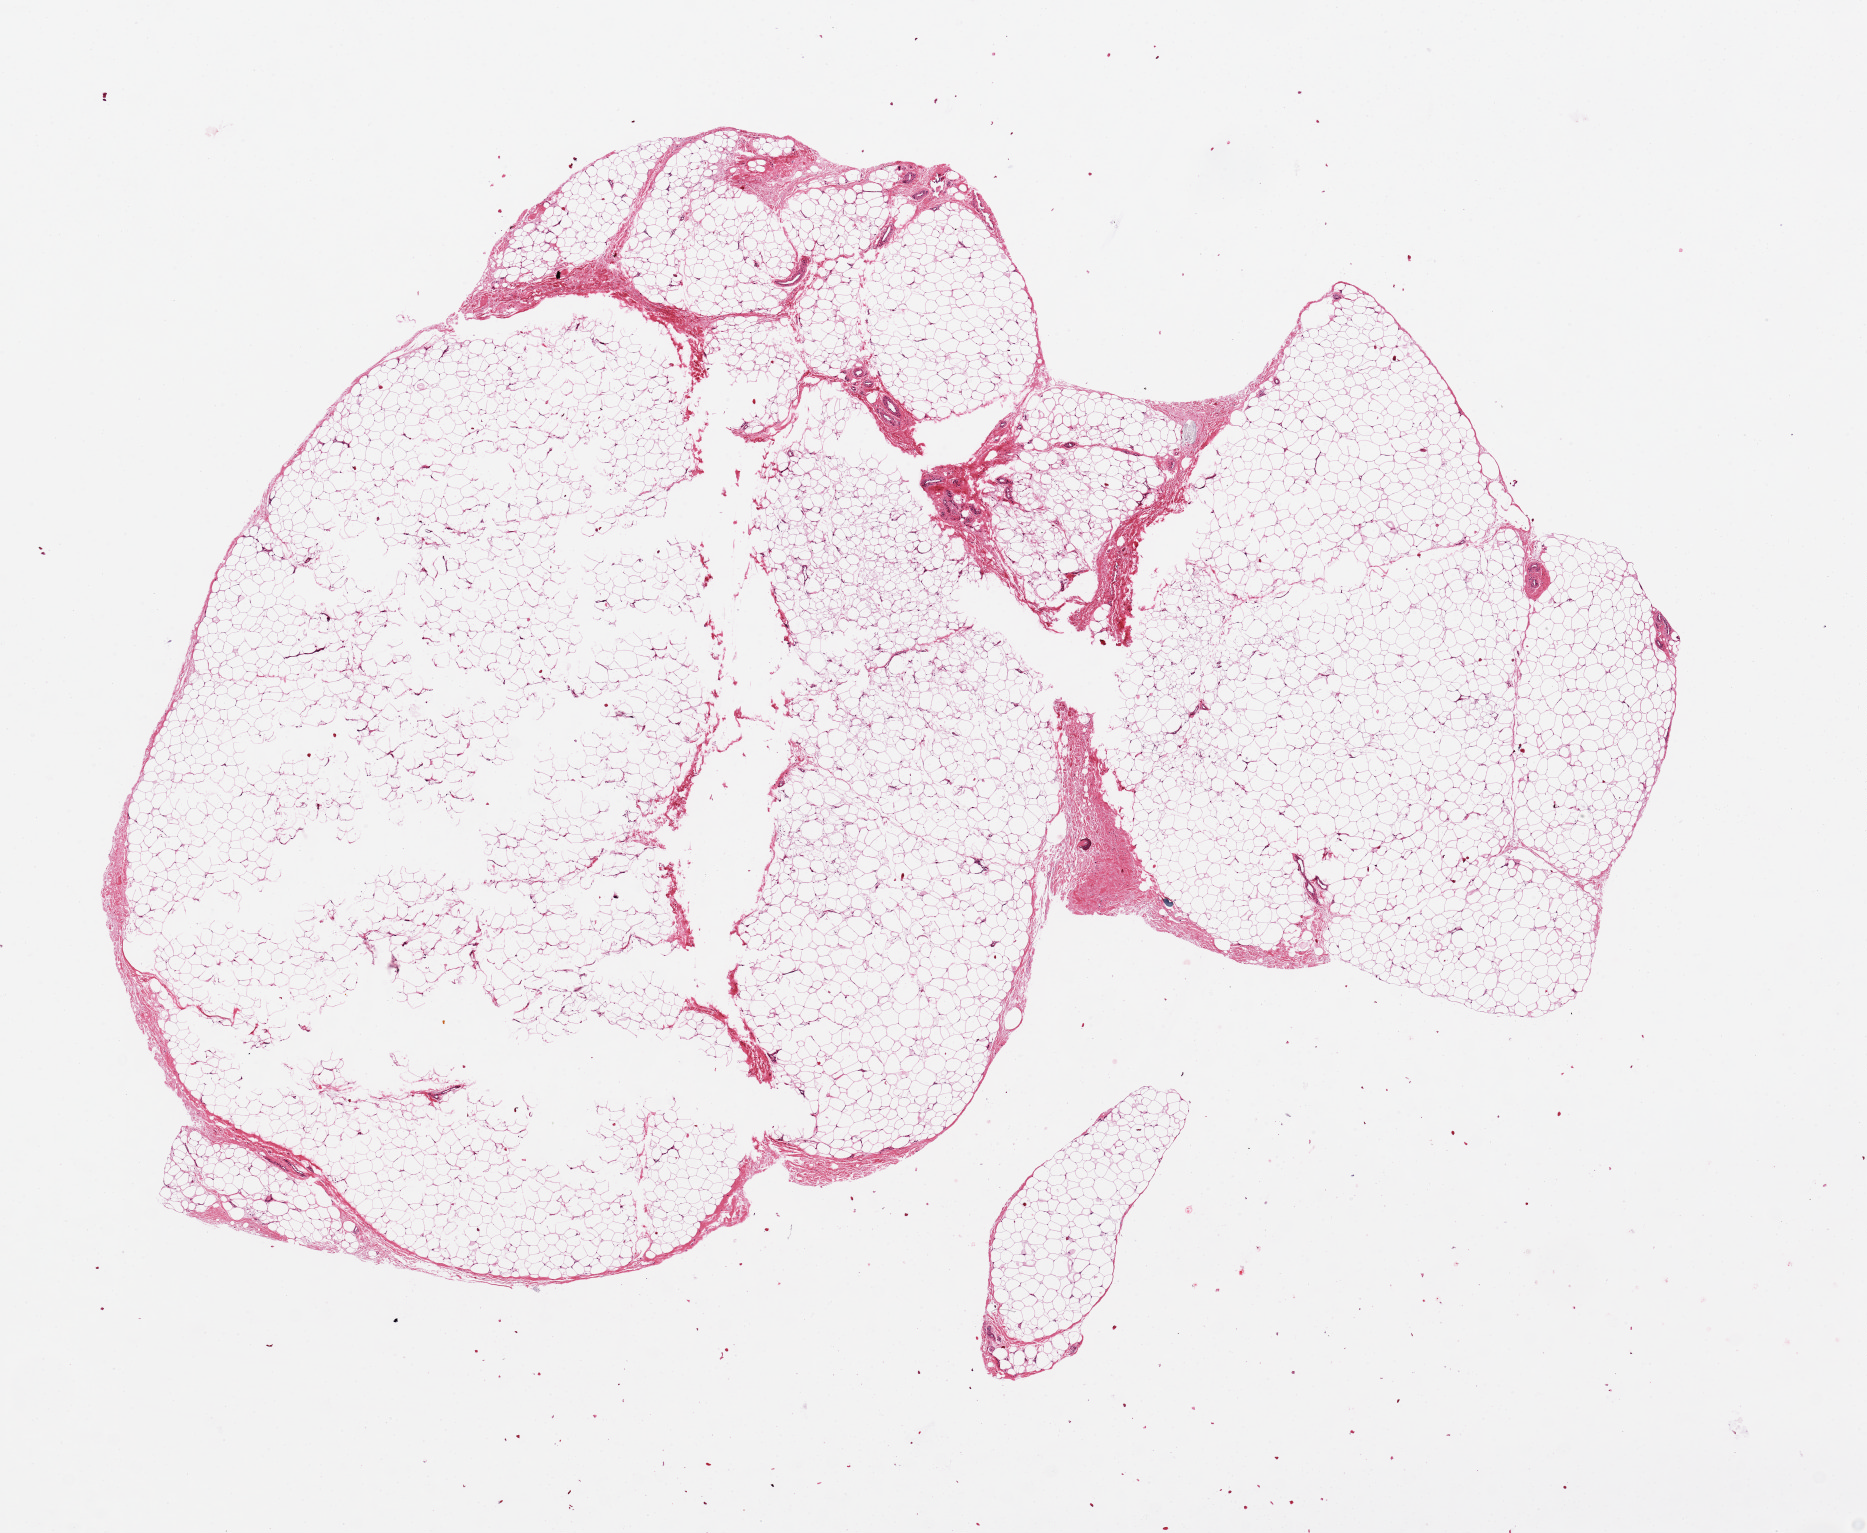
Haematoxylin and eosin whole-slide image — a low-resolution overview of the entire scanned area, about 14.8 x 12.1 mm (acquisition: 20x scan); PAXgene-fixed, paraffin-embedded tissue; section of adipose tissue (target tissue); tissue donor sample.
* pathologist's review note for this sample: Central 10% hollow. 12 x 9mm